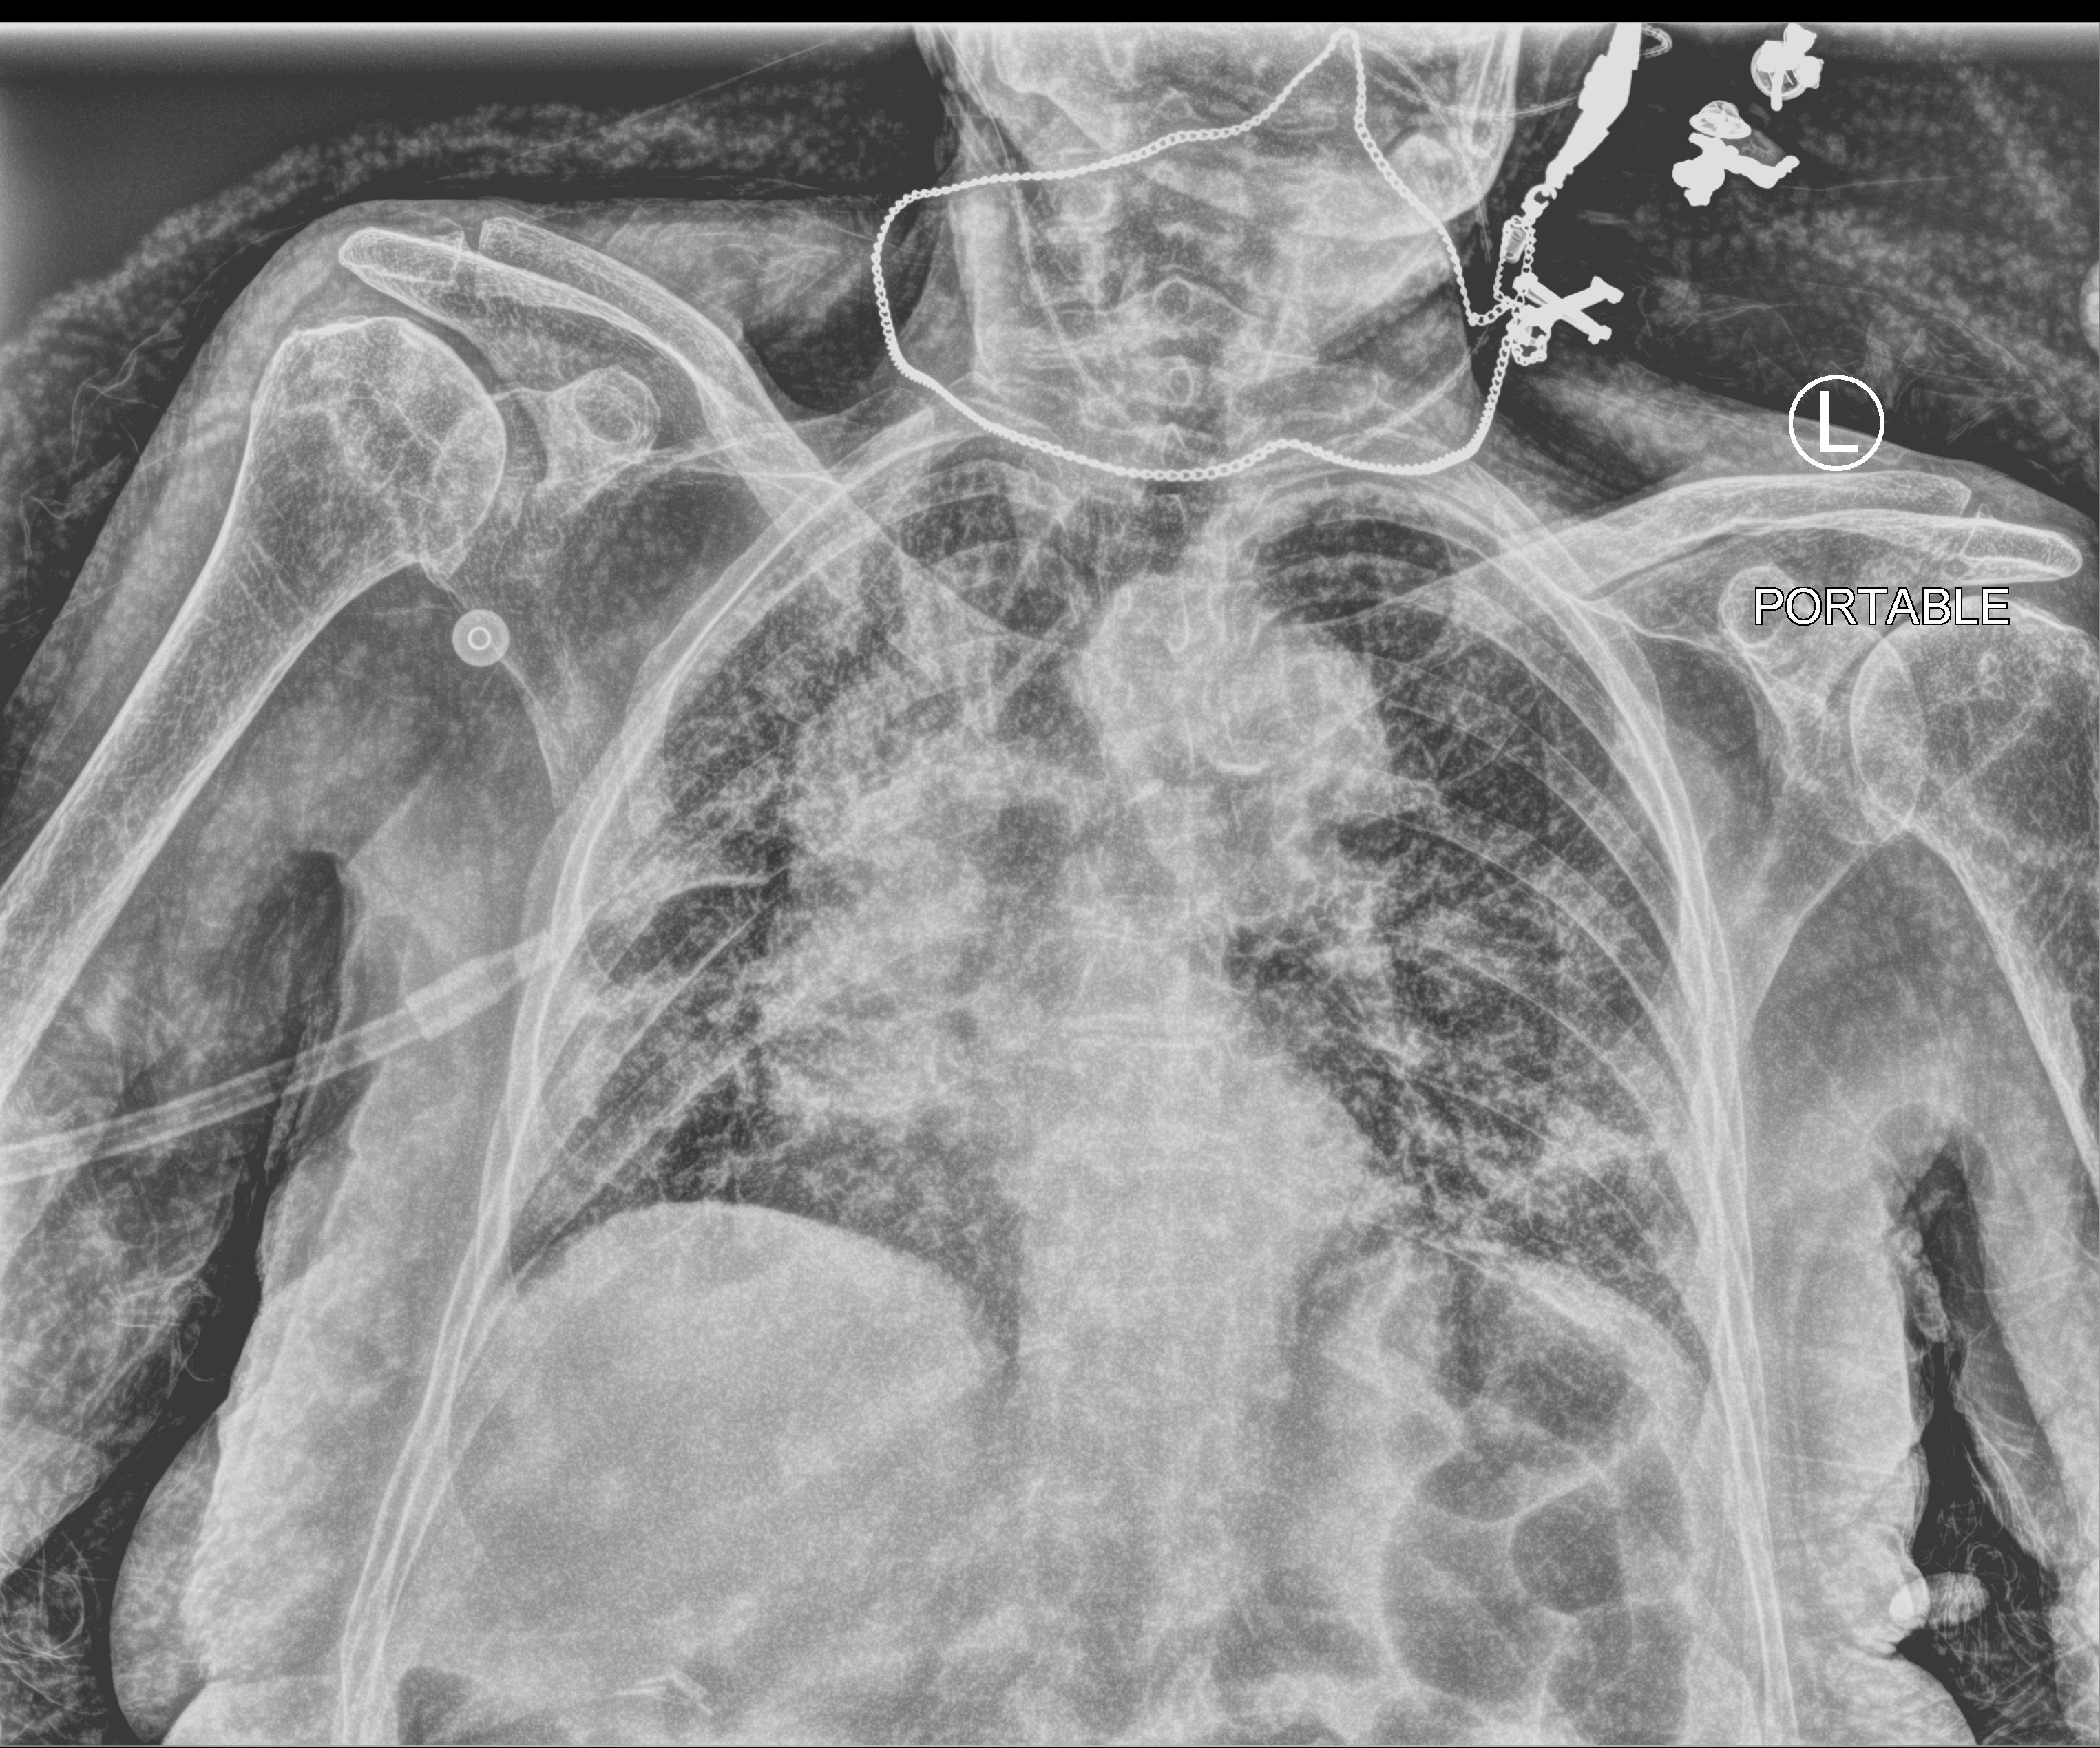
Portable chest radiograph; anteroposterior (AP) projection. Female patient hospitalised with COVID-19, age 75–90 years.
From the hospital-stay record, not from the radiograph (when in the stay this image was taken is not recorded): mechanically ventilated during this hospital stay: no; admitted to intensive care during this hospital stay: no.